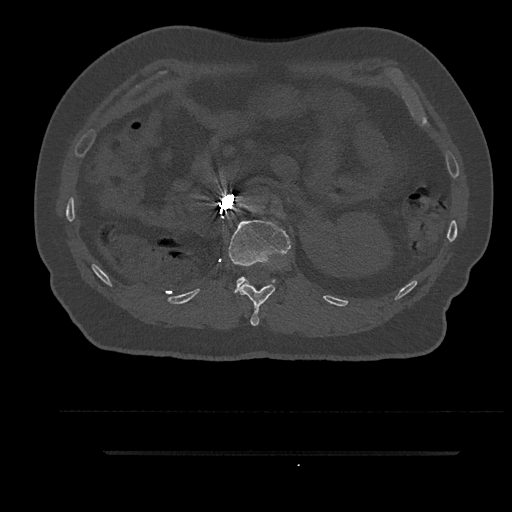
CT including the spine, one axial slice. Position 207 of 797 along the scan axis. 120 kVp. Bone window (W 1800 / L 400 HU). 0.5 mm slice thickness. 512 × 512 image matrix. Patient: male, 63 years. From the clinical record (not read from this slice): primary cancer: renal; vertebrae with lytic lesions (as recorded): T8.
Outlined on this slice (semi-automatically segmented with operator editing):
- L1 vertebra: bounding box <228,220,291,294> (left, top, right, bottom; pixels)
- T12 vertebra: <239,281,275,326>